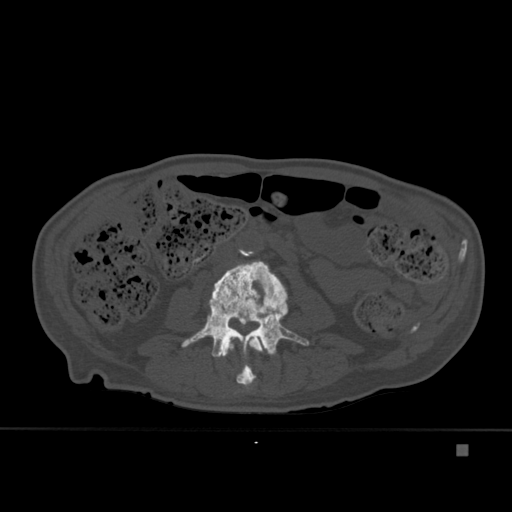
CT including the spine, one axial slice. Position 145 of 451 along the scan axis. Bone window (W 1800 / L 400 HU). 512 × 512 image matrix, field of view 378 × 378 mm. Patient: male, 75 years. Case-level facts recorded for this patient, not image findings: primary cancer: prostate.
Structures marked on this image (semi-automatically segmented with operator editing):
- L2 vertebra: bounding box [x1, y1, x2, y2] px = [221, 336, 263, 389]
- L3 vertebra: [181, 260, 309, 383]